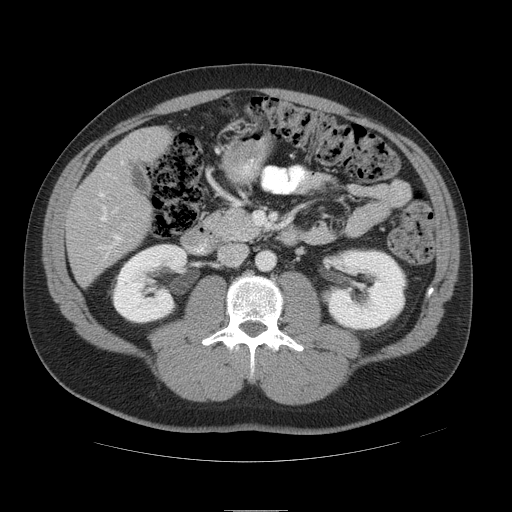
Contrast-enhanced abdominal CT, one axial slice; reconstruction kernel STANDARD; 120 kVp; intravenous contrast given; soft-tissue window (W 400 / L 40 HU); 5 mm slice thickness; 512 × 512 image matrix. Male patient, age 52 years. From the clinical record (not read from this slice): diagnosis: colorectal cancer liver metastases, imaged before liver resection; multiple liver metastases: yes; largest metastasis: 5.1 cm; disease in both lobes: yes.
Outlined on this slice (expert manual segmentation):
- hepatic veins: bounding box [x1, y1, x2, y2] px = [100, 206, 107, 221]
- liver: [68, 128, 167, 284]
- planned liver remnant (the part of the liver to remain after resection): [134, 128, 168, 155]
- portal vein (with intrahepatic branches): [97, 173, 123, 259]